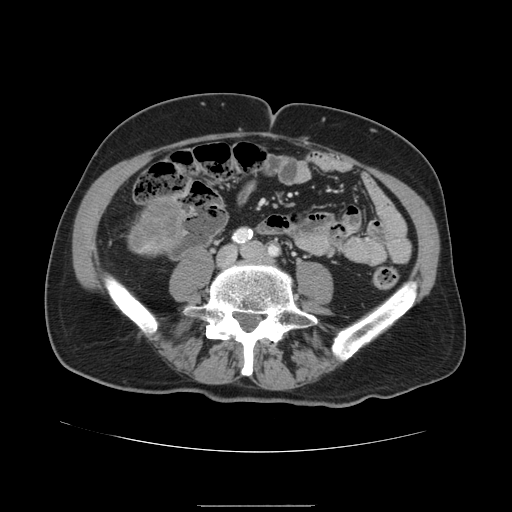
Contrast-enhanced abdominal CT, one axial slice. Position 9 of 168 along the scan axis. Intravenous contrast given. Soft-tissue window (W 400 / L 40 HU). 2.5 mm slice thickness. 512 × 512 image matrix, field of view 386 × 386 mm. Male patient, age 74 years. Case-level facts recorded for this patient, not image findings: diagnosis: colorectal cancer liver metastases, imaged before liver resection; multiple liver metastases: no; largest metastasis: 14.5 cm.
Annotated regions visible in this slice (manually delineated by an expert):
- liver: bounding box [x1, y1, x2, y2] px = [128, 196, 188, 257]
- liver metastasis: [129, 199, 181, 249]